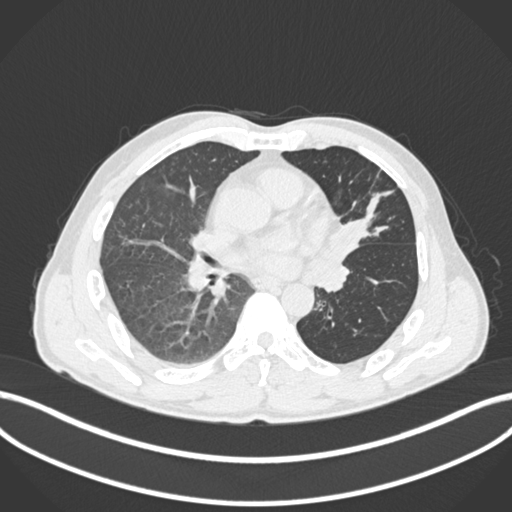
Chest CT, one axial slice; slice 91 of 255 in the series (ordered by position); 120 kVp; lung window (W 1500 / L -600 HU); 1 mm slice thickness; 512 × 512 image matrix, field of view 400 × 400 mm. Male patient, age 57 years. From the clinical record (not read from this slice): clinical TNM (as recorded): T2b N0 M0.
Structures marked on this image (rectangle marked by the reading radiologist):
- lung tumour (recorded histology: squamous cell carcinoma): box from (x=321, y=207) to (x=370, y=283) px